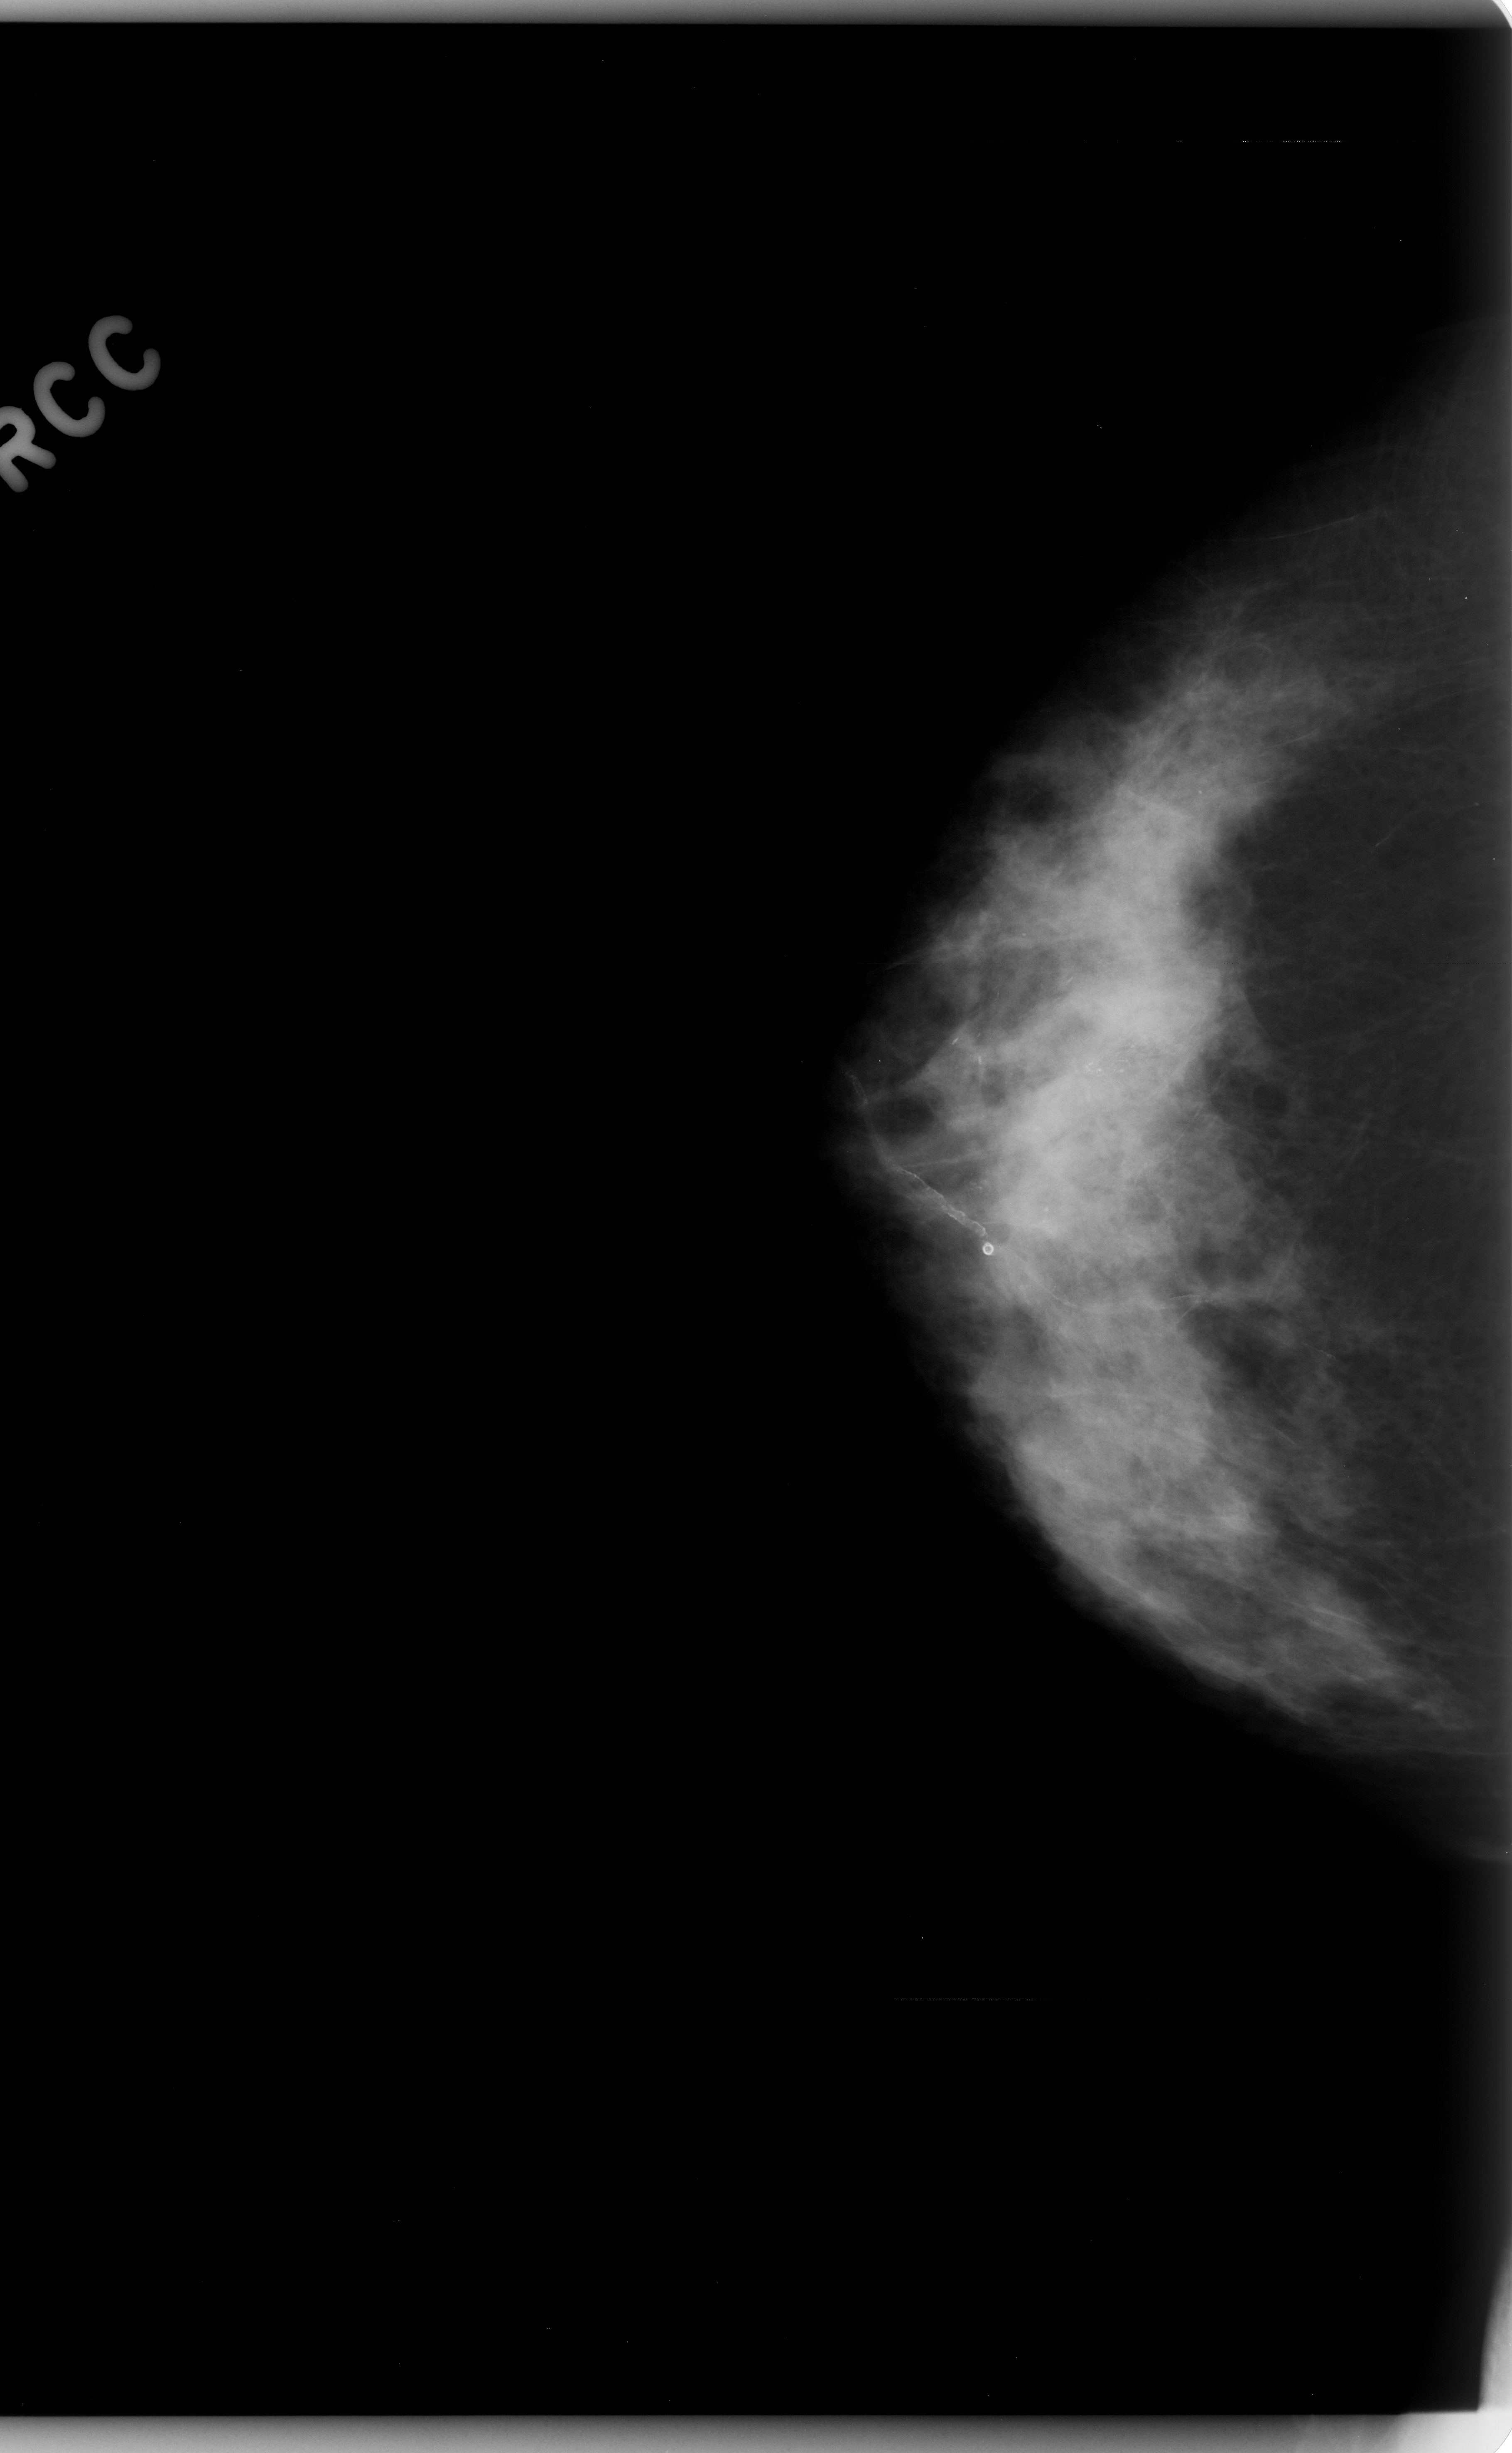
Digitized screen-film mammogram. Right breast. Craniocaudal (CC) view. BI-RADS breast density category 3 (scale 1–4). 1512 × 2453 image matrix.
Expert-marked regions of interest on this image (one box per marked abnormality):
- calcifications, morphology fine linear branching, distribution segmental; BI-RADS assessment category 5; pathology (as recorded): malignant: bounding box [x1, y1, x2, y2] px = [917, 1003, 1237, 1148]